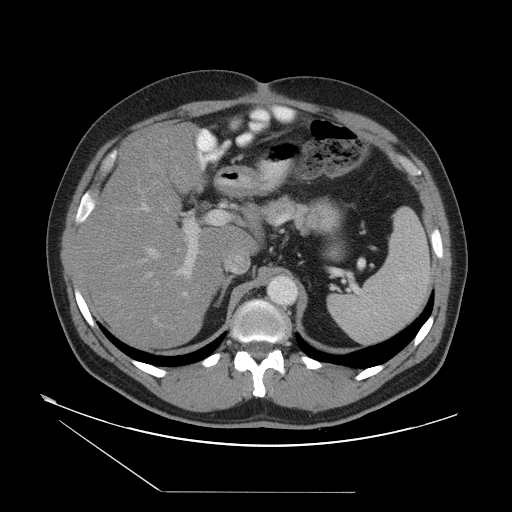
Contrast-enhanced abdominal CT, one axial slice; position 31 of 55 along the scan axis; reconstruction kernel STANDARD; 120 kVp; intravenous contrast given; soft-tissue window (W 400 / L 40 HU); 5 mm slice thickness; 512 × 512 image matrix. Male patient, age 59 years. From the clinical record (not read from this slice): diagnosis: colorectal cancer liver metastases, imaged before liver resection; multiple liver metastases: yes; largest metastasis: 0.3 cm; disease in both lobes: yes.
Annotated regions visible in this slice (expert manual segmentation):
- hepatic veins: bounding box <138,136,204,322> (left, top, right, bottom; pixels)
- liver: <83,124,255,350>
- planned liver remnant (the part of the liver to remain after resection): <83,138,255,350>
- portal vein (with intrahepatic branches): <137,141,231,296>